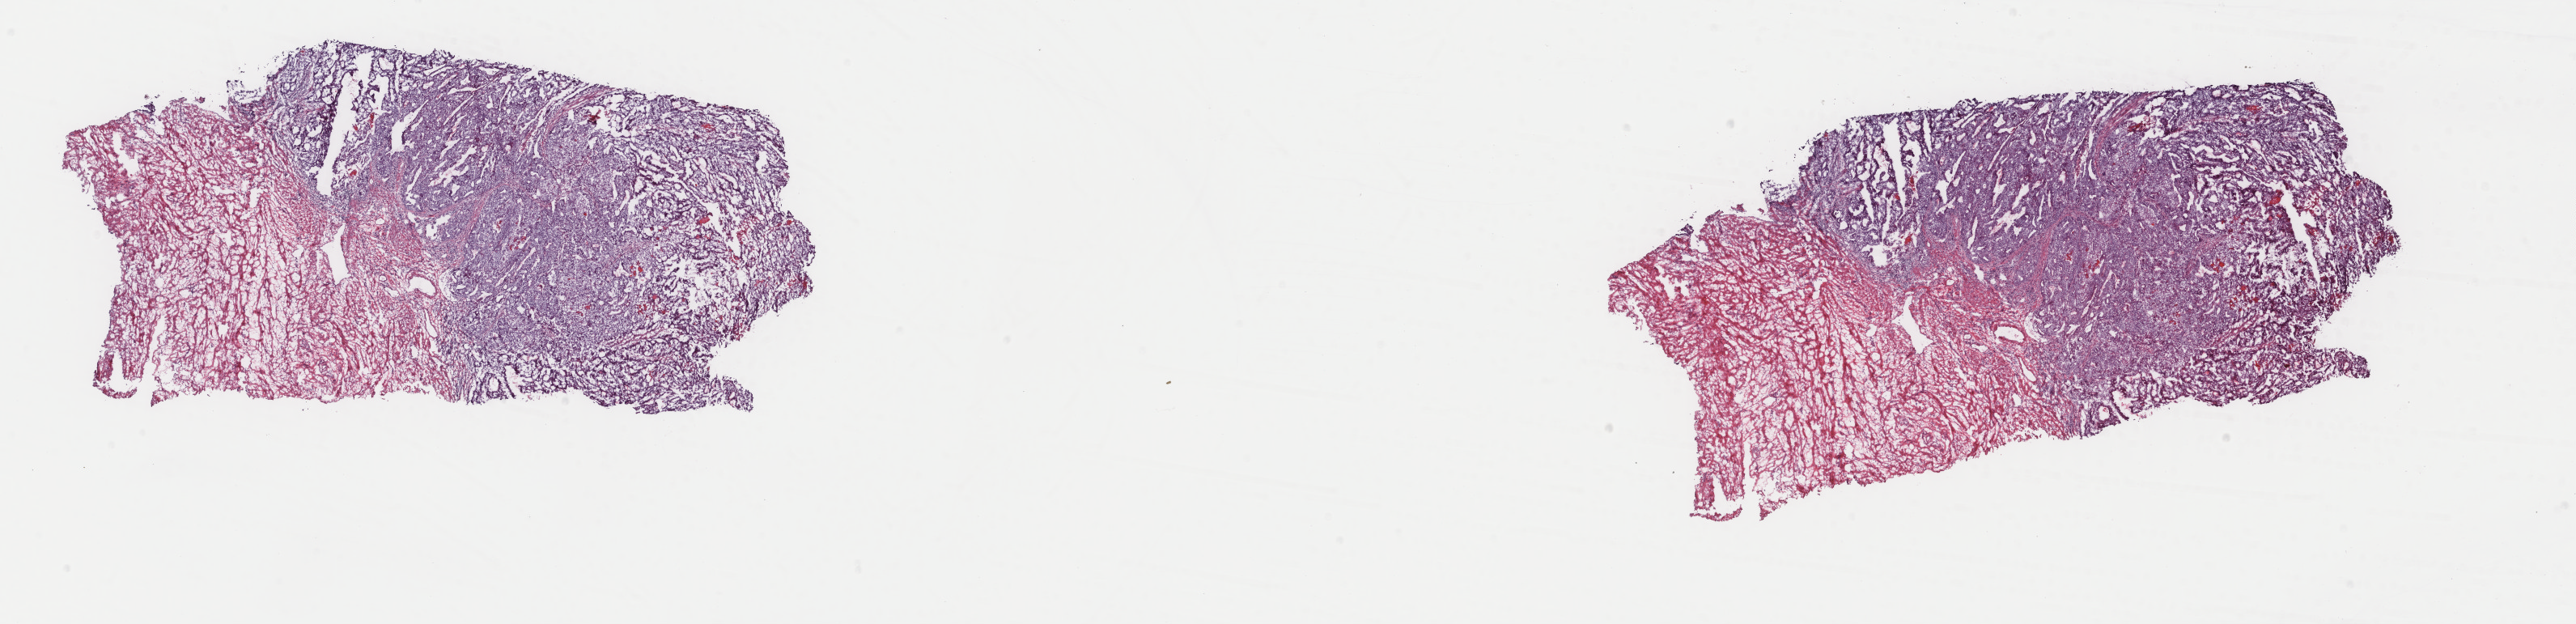
Whole-slide histology image, H&E, a low-resolution overview of the entire scanned area, about 25.3 x 6.1 mm, frozen section, primary tumour sample from the uterus. Female, age 71 years at initial diagnosis. Histologic grade: G3 (poorly differentiated). Slide review estimates, as recorded: tumour cells 60%, tumour nuclei 60%, normal cells 0%, stromal cells 40%, necrosis 0%. Infiltration values recorded for this section: lymphocyte infiltration 20%, monocyte infiltration 40%, neutrophil infiltration 20%.
Histologic diagnosis: Endometrioid adenocarcinoma, NOS (endometrium). FIGO stage: IIIB.